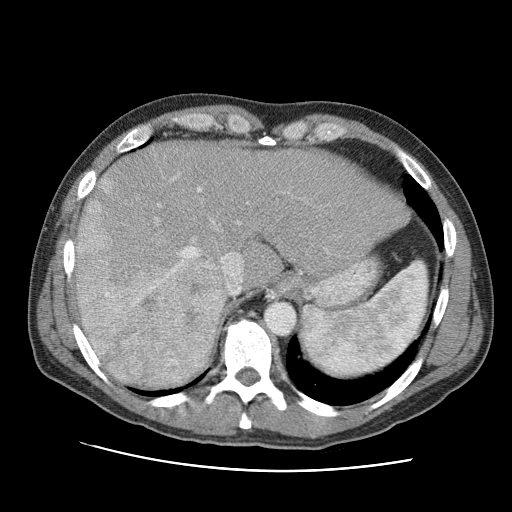
Contrast-enhanced abdominal CT (liver protocol), one axial slice; position 74 of 95 along the scan axis; reconstruction kernel STANDARD; 120 kVp; one of 2 acquisitions stored at this slice position; soft-tissue window (W 400 / L 40 HU); 512 × 512 image matrix. Case-level facts recorded for this patient, not image findings: diagnosis: hepatocellular carcinoma (patient treated with transarterial chemoembolisation; whether this scan precedes or follows treatment is not stated here); TNM stage (as recorded): Stage-IVA; Child-Pugh class: A; tumour differentiation: moderately differentiated; tumour nodularity: multinodular.
Structures marked on this image (semi-automatically segmented with operator editing):
- liver parenchyma outside the tumour (the mass and vessels are separate outlines, so this box may not span the whole liver): bounding box (x1, y1, x2, y2) in pixels: (76, 142, 408, 384)
- mass: (74, 176, 228, 388)
- liver vessels: (155, 187, 241, 261)